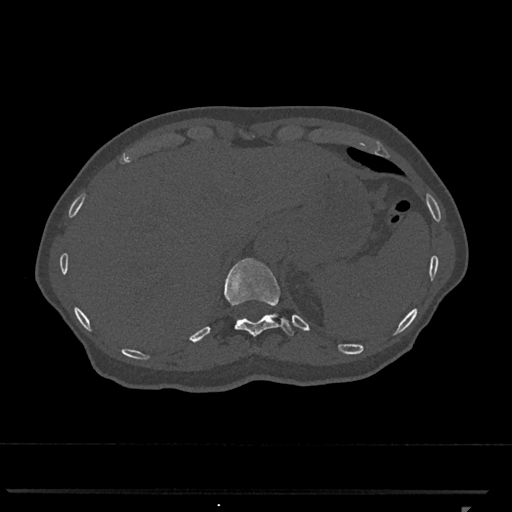
CT including the spine, one axial slice. Position 514 of 793 along the scan axis. Reconstruction kernel Br40s/3. Bone window (W 1800 / L 400 HU). 0.5 mm slice thickness. 512 × 512 image matrix, field of view 380 × 380 mm. Patient: female, 62 years. From the clinical record (not read from this slice): primary cancer: renal.
Annotated regions visible in this slice (semi-automatically segmented with operator editing):
- T11 vertebra: bounding box (x1, y1, x2, y2) in pixels: (224, 258, 294, 337)